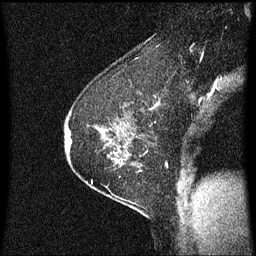
Breast MRI (dynamic contrast-enhanced), one sagittal slice; position 45 of 60 along the scan axis; dynamic contrast-enhanced series, image 2 of 3 at this slice position (ordered by acquisition); 1.5 T; TE 4.2 ms, TR 8.4 ms; 2 mm slice thickness; 256 × 256 image matrix, field of view 200 × 200 mm. Female patient, age 60 years.
Annotated regions visible in this slice (semi-automatic segmentation, software-assisted and operator-edited):
- analysis volume of interest (the breast-tissue region the enhancement analysis was run in; not a lesion): box from (x=69, y=66) to (x=146, y=193) px
- tumour enhancement mask (voxels above the 70 % enhancement threshold inside the analysis volume of interest): (x=69, y=128)–(x=125, y=165)